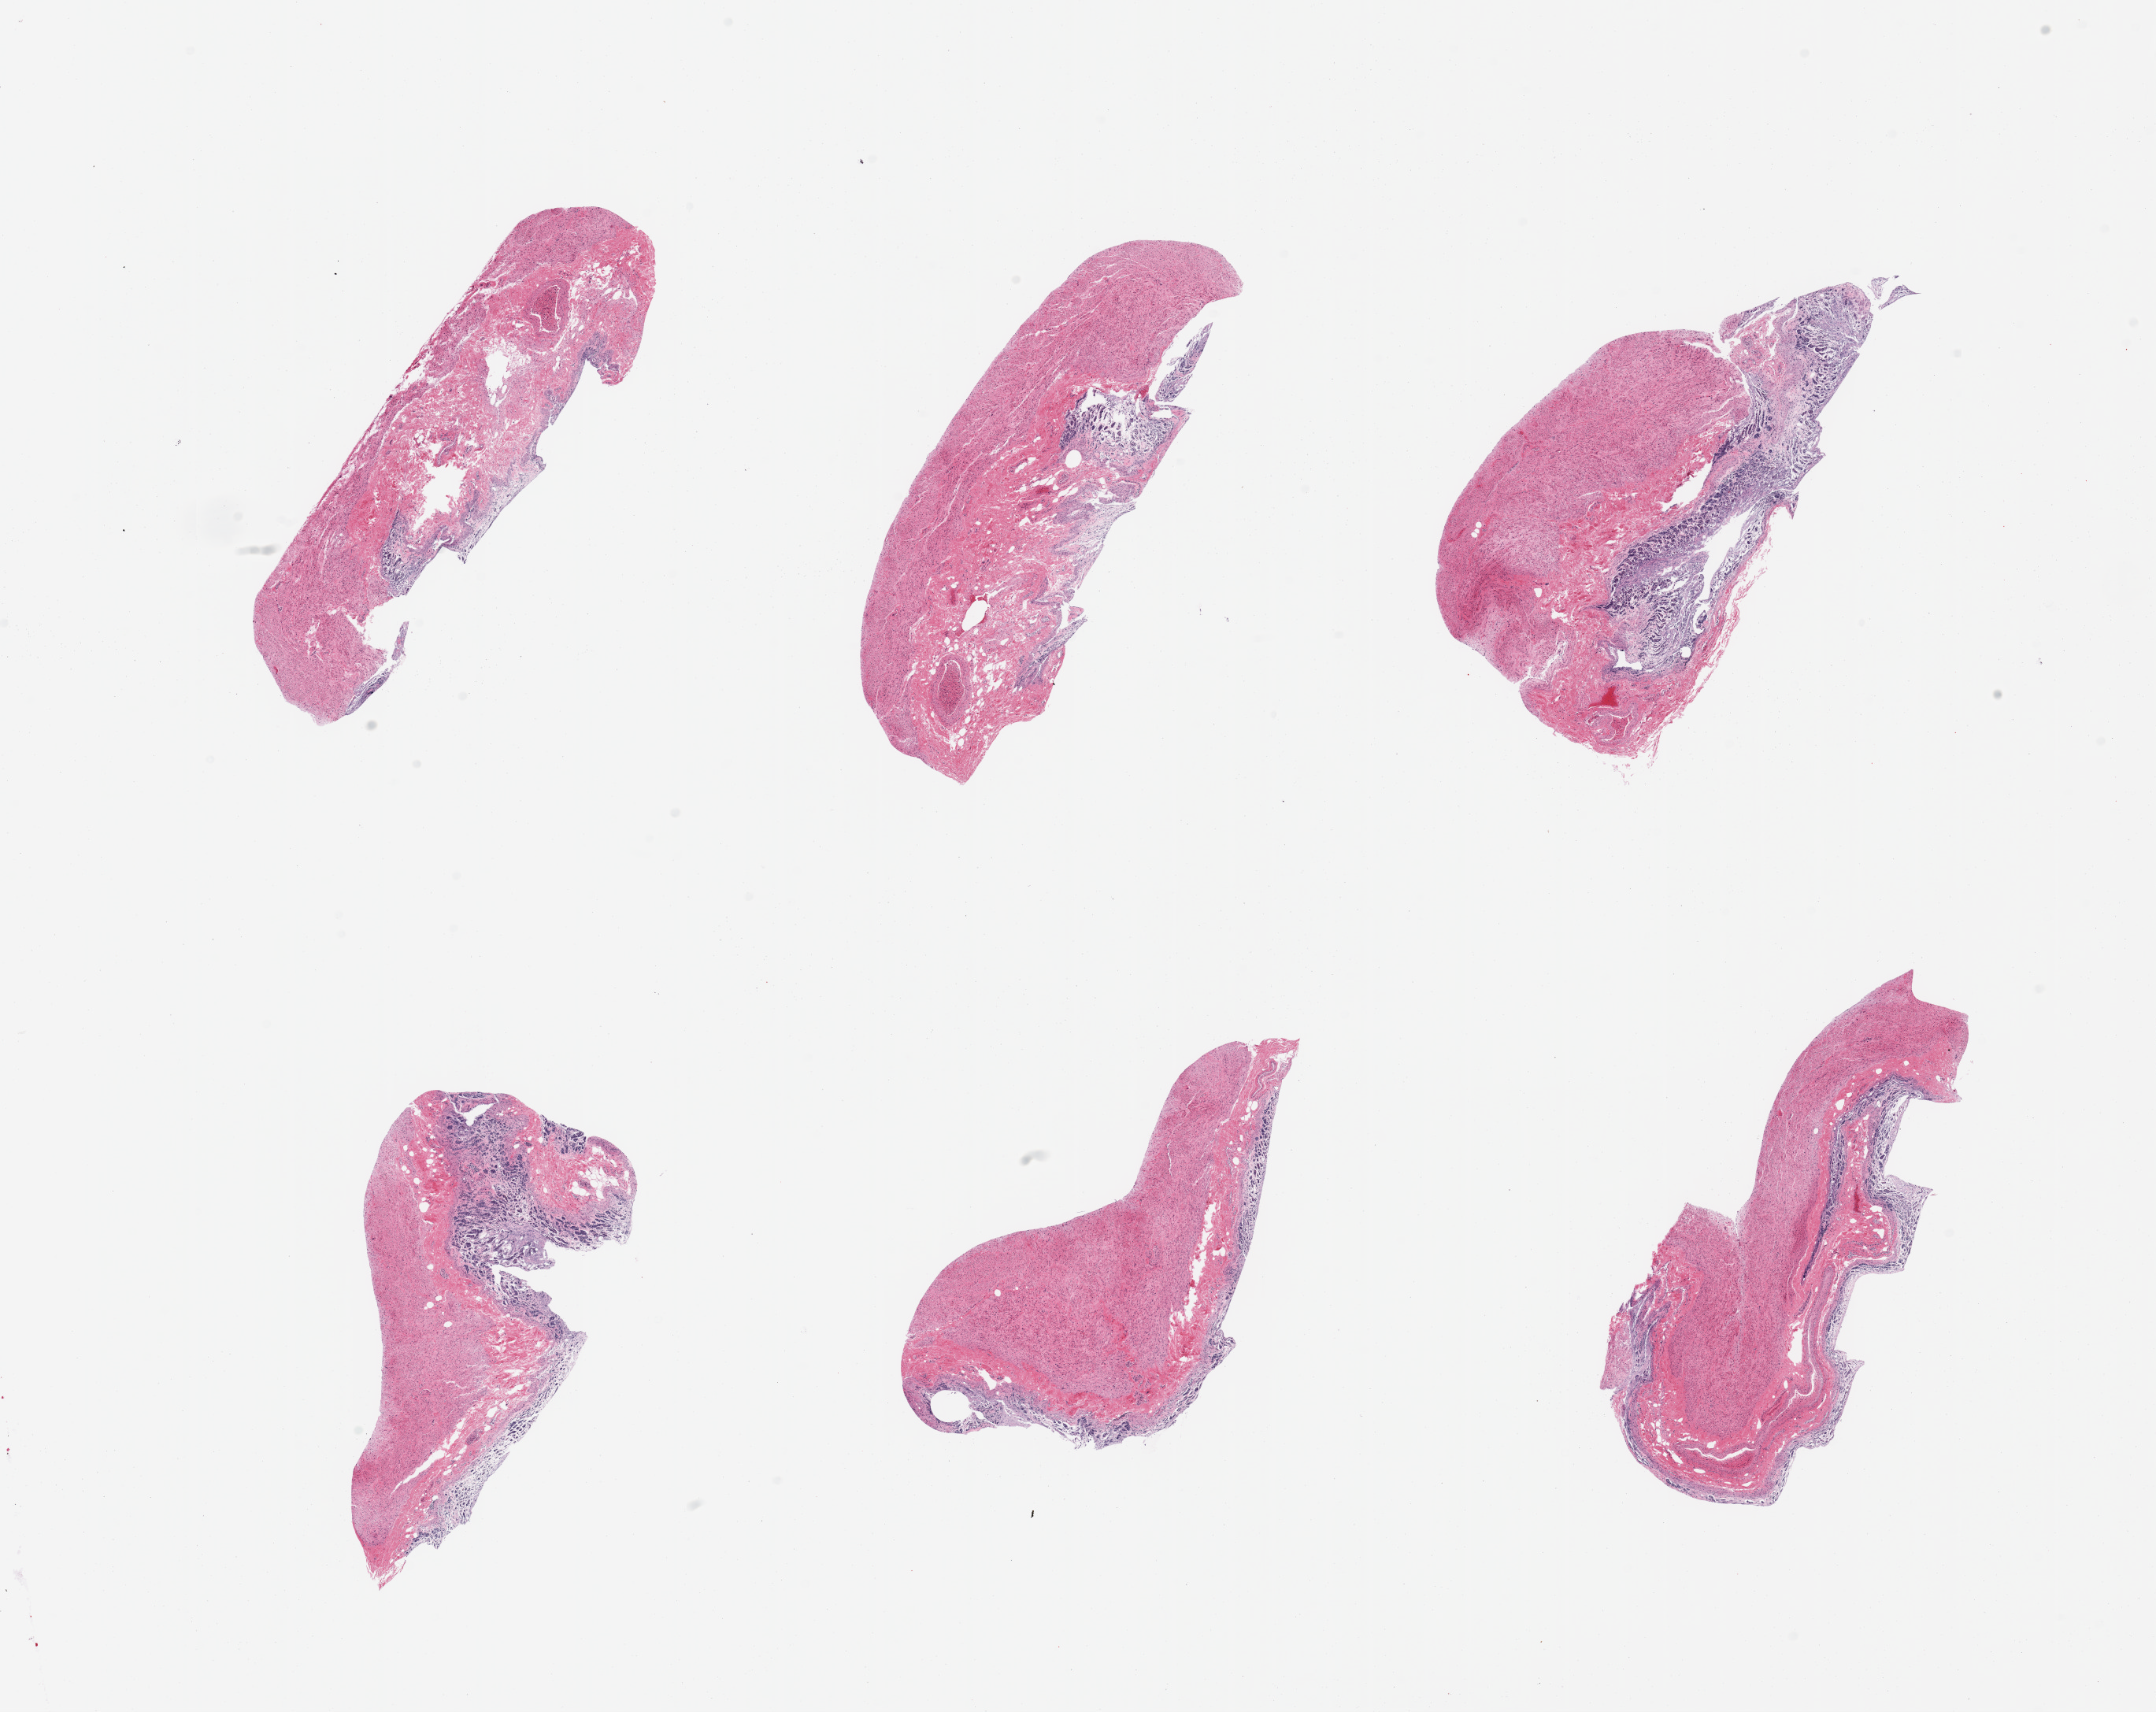
Whole-slide image, H&E stain, whole scanned area (about 21.7 x 17.2 mm) shown as a low-resolution overview, PAXgene-fixed, paraffin-embedded tissue, target tissue: stomach, tissue donor sample. Donor sex: male.
- review note (as recorded): 6 pieces, target mucosa up to ~0.5mm, sloughing, advanced autolysis